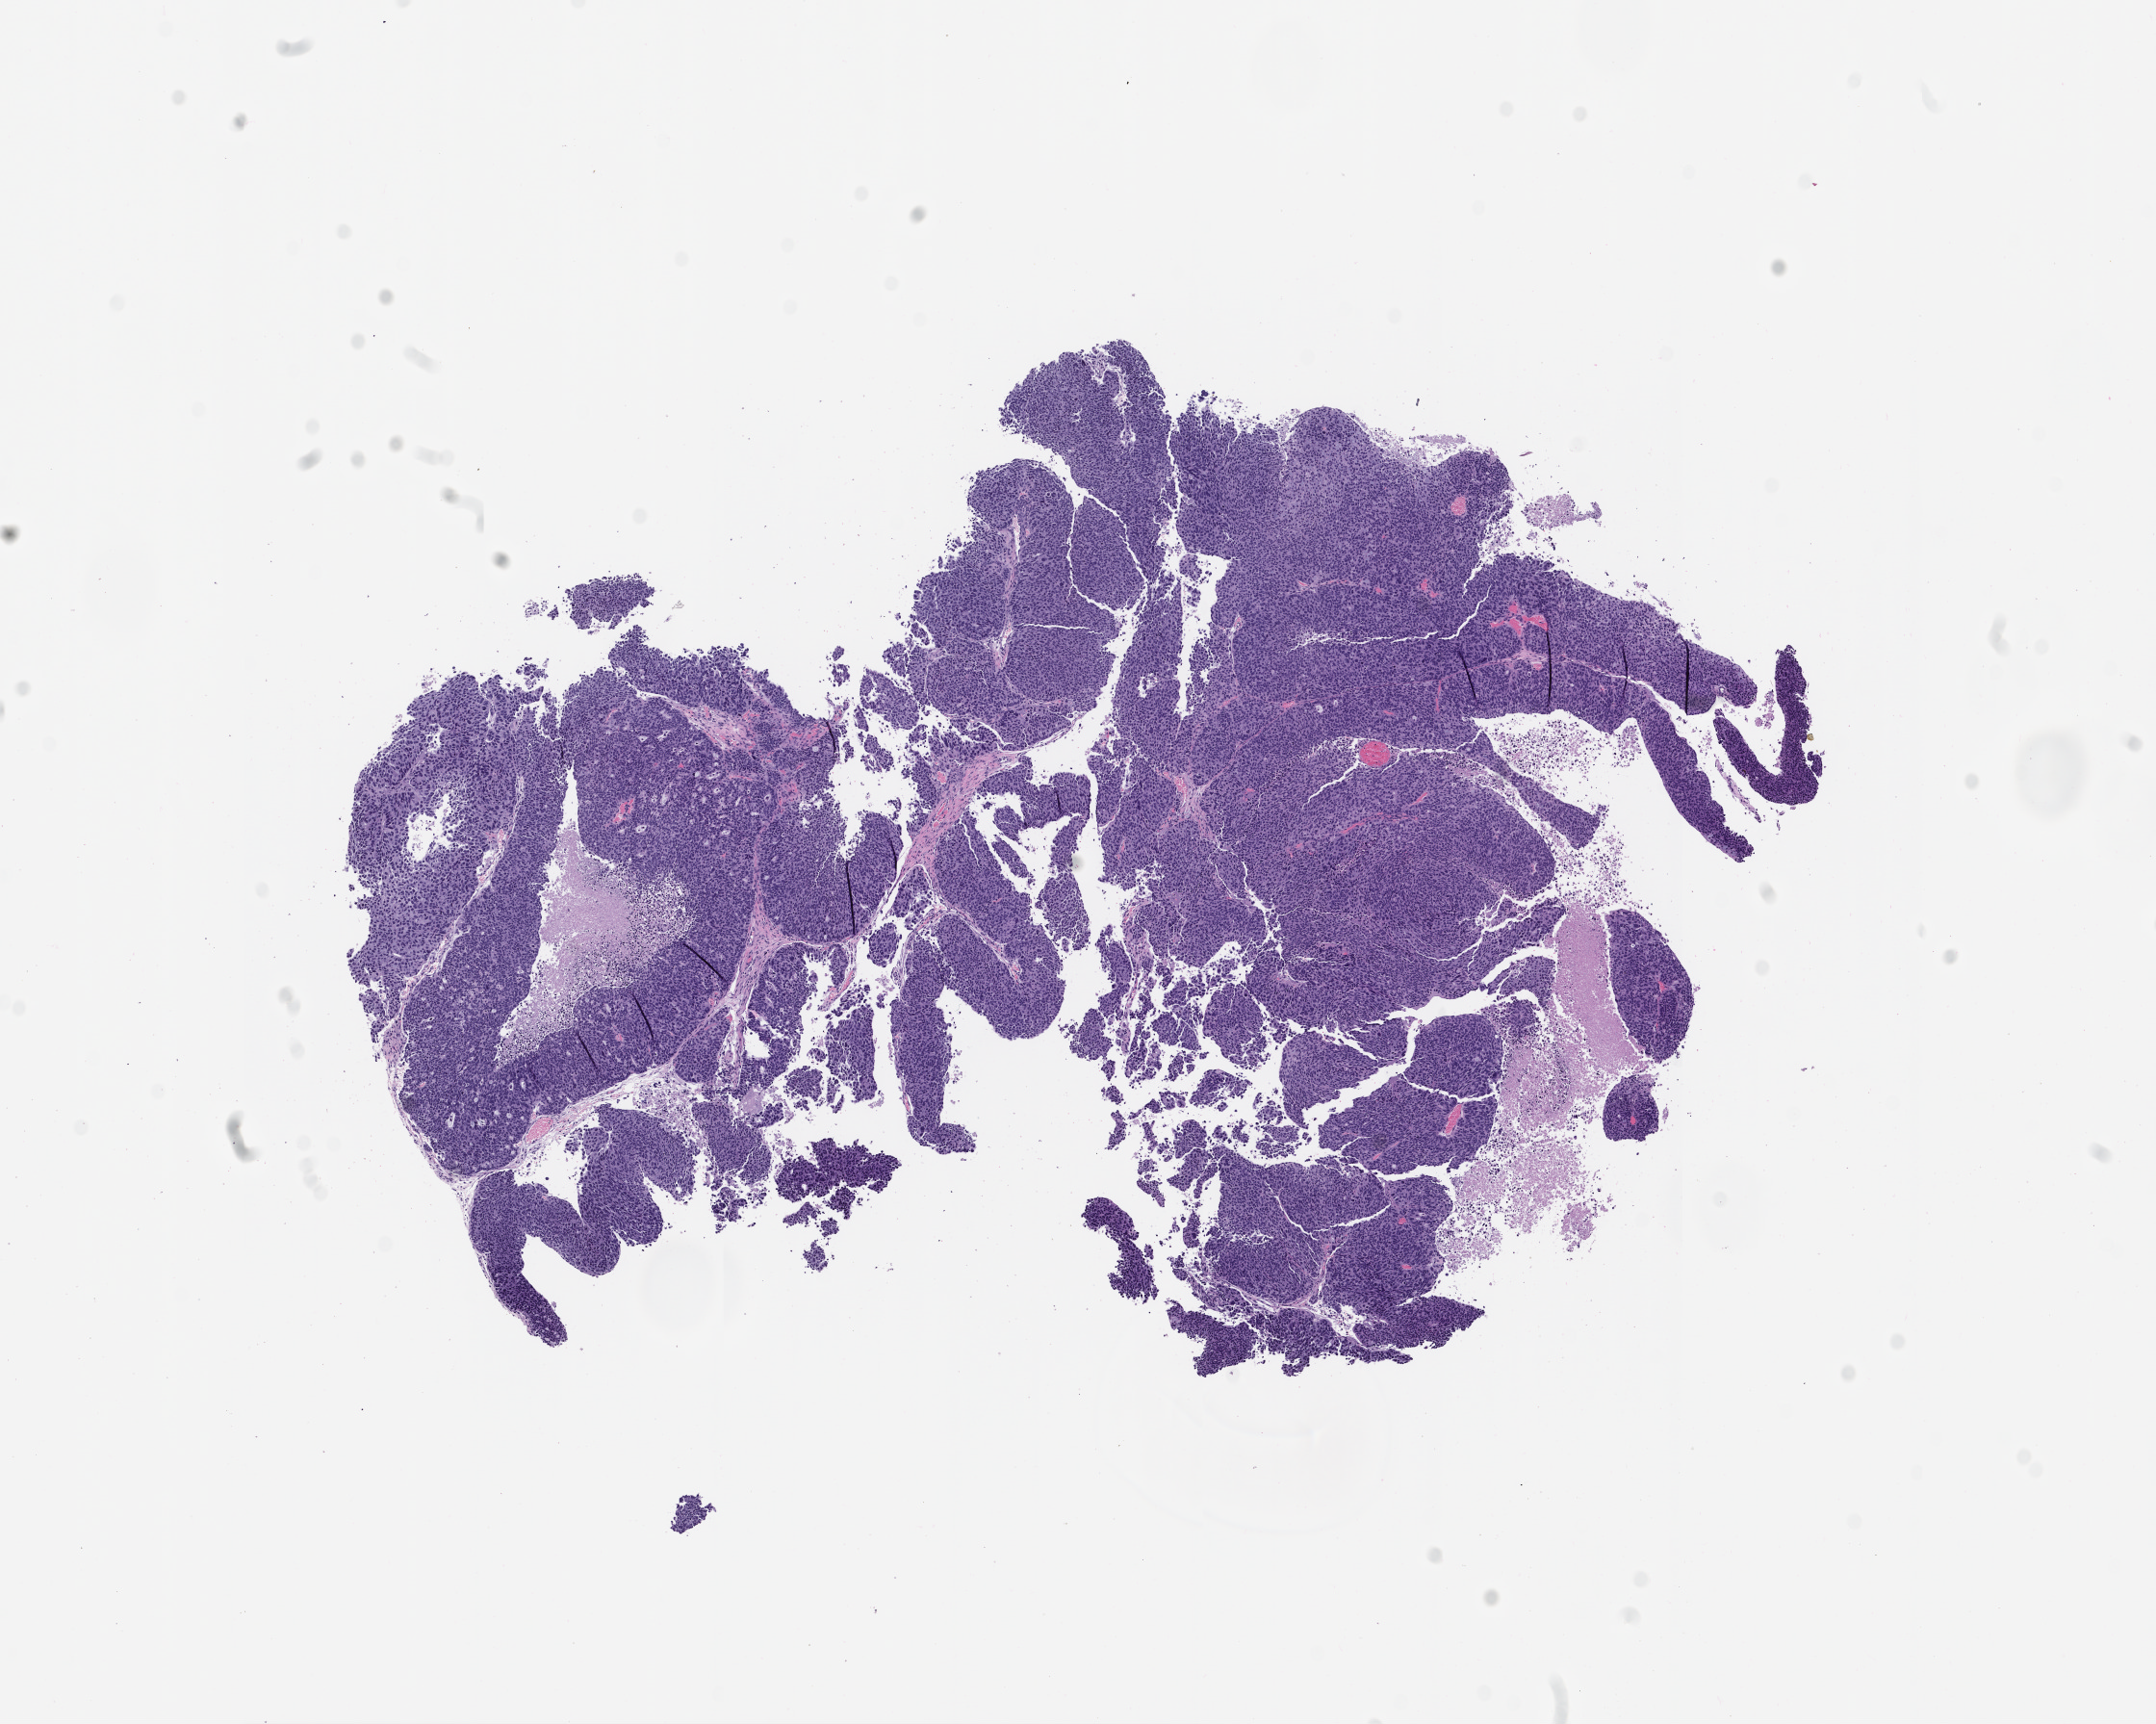
Whole-slide image, hematoxylin and eosin (H&E): patient-derived xenograft (human tumor grown in a mouse), passage 4, low-resolution overview of the scanned area, about 9.0 x 7.2 mm, formalin-fixed paraffin-embedded section, originating tumor site category: gastrointestinal tract.
Originating patient diagnosis: Gastric Adenocarcinoma.